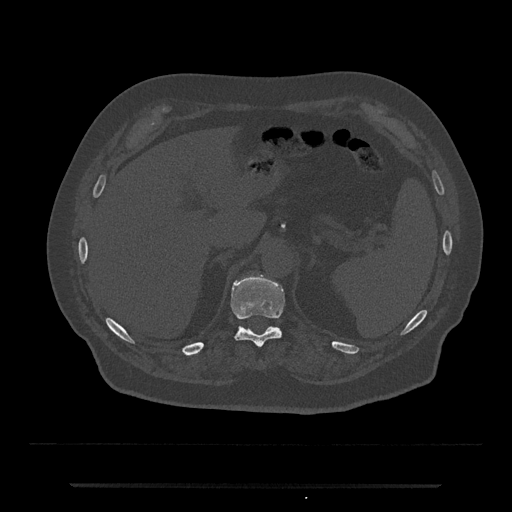
CT including the spine, one axial slice. Position 646 of 797 along the scan axis. Reconstruction kernel Br40s/3. 120 kVp. Bone window (W 1800 / L 400 HU). 0.5 mm slice thickness. 512 × 512 image matrix. Male patient, age 80 years. Case-level facts recorded for this patient, not image findings: primary cancer: prostate.
Structures marked on this image (semi-automatically segmented with operator editing):
- T11 vertebra: bounding box [x1, y1, x2, y2] px = [230, 276, 285, 348]